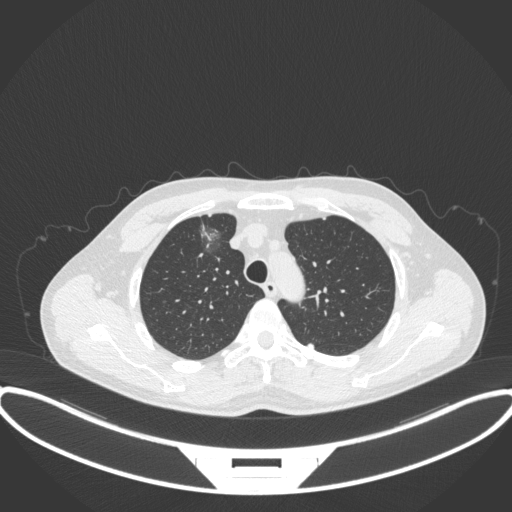
Chest CT, one axial slice; position 285 of 395 along the scan axis; reconstruction kernel B31f; 120 kVp; lung window (W 1500 / L -600 HU); 1 mm slice thickness; 512 × 512 image matrix. Male patient, age 60 years. From the clinical record (not read from this slice): clinical TNM (as recorded): T1c N0 M0.
Outlined on this slice (rectangle marked by the reading radiologist):
- lung tumour (recorded histology: adenocarcinoma): bounding box (x1, y1, x2, y2) in pixels: (196, 218, 227, 256)